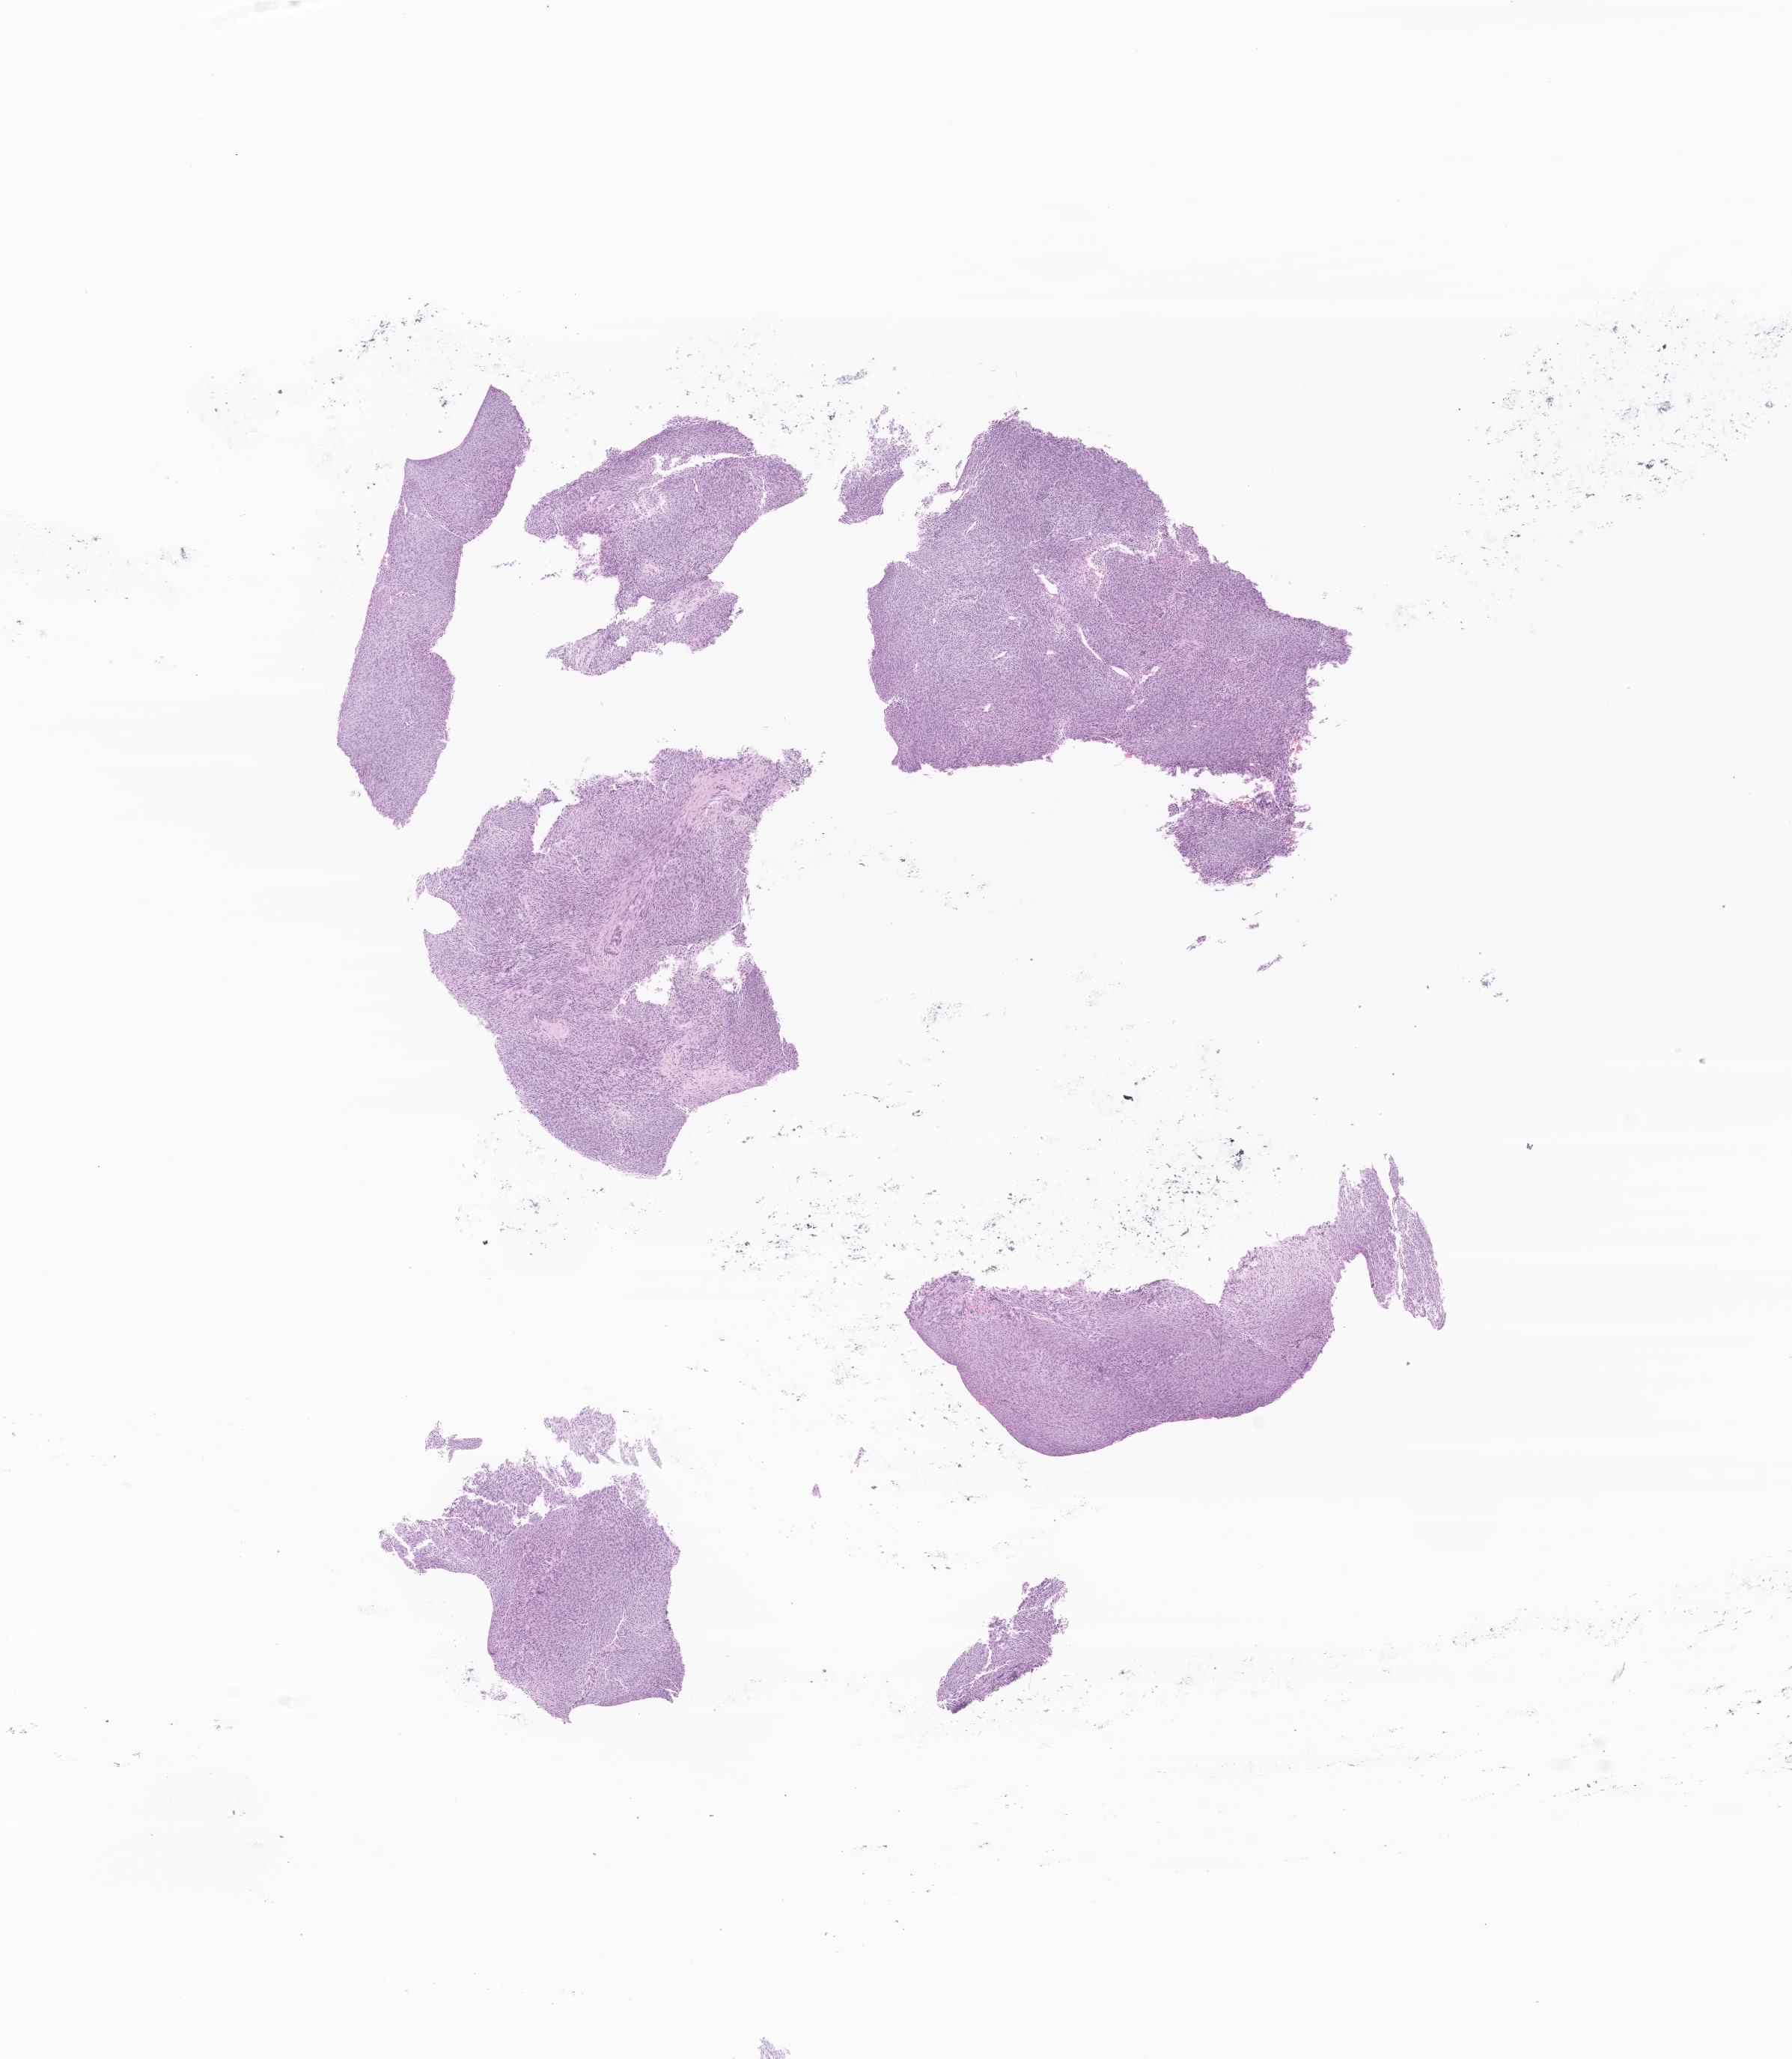
Digitized hematoxylin and eosin (H&E)-stained section of tumor tissue from the soft tissue of lower extremity, a low-resolution overview of the entire scanned area, about 10.1 x 11.6 mm. Formalin-fixed, paraffin-embedded (FFPE) tissue. Male patient, age 121 days.
Tissue or organ of origin (case record): connective, subcutaneous and other soft tissues of lower limb and hip. Diagnosis (ICD-O-3 morphology term): Infantile fibrosarcoma.